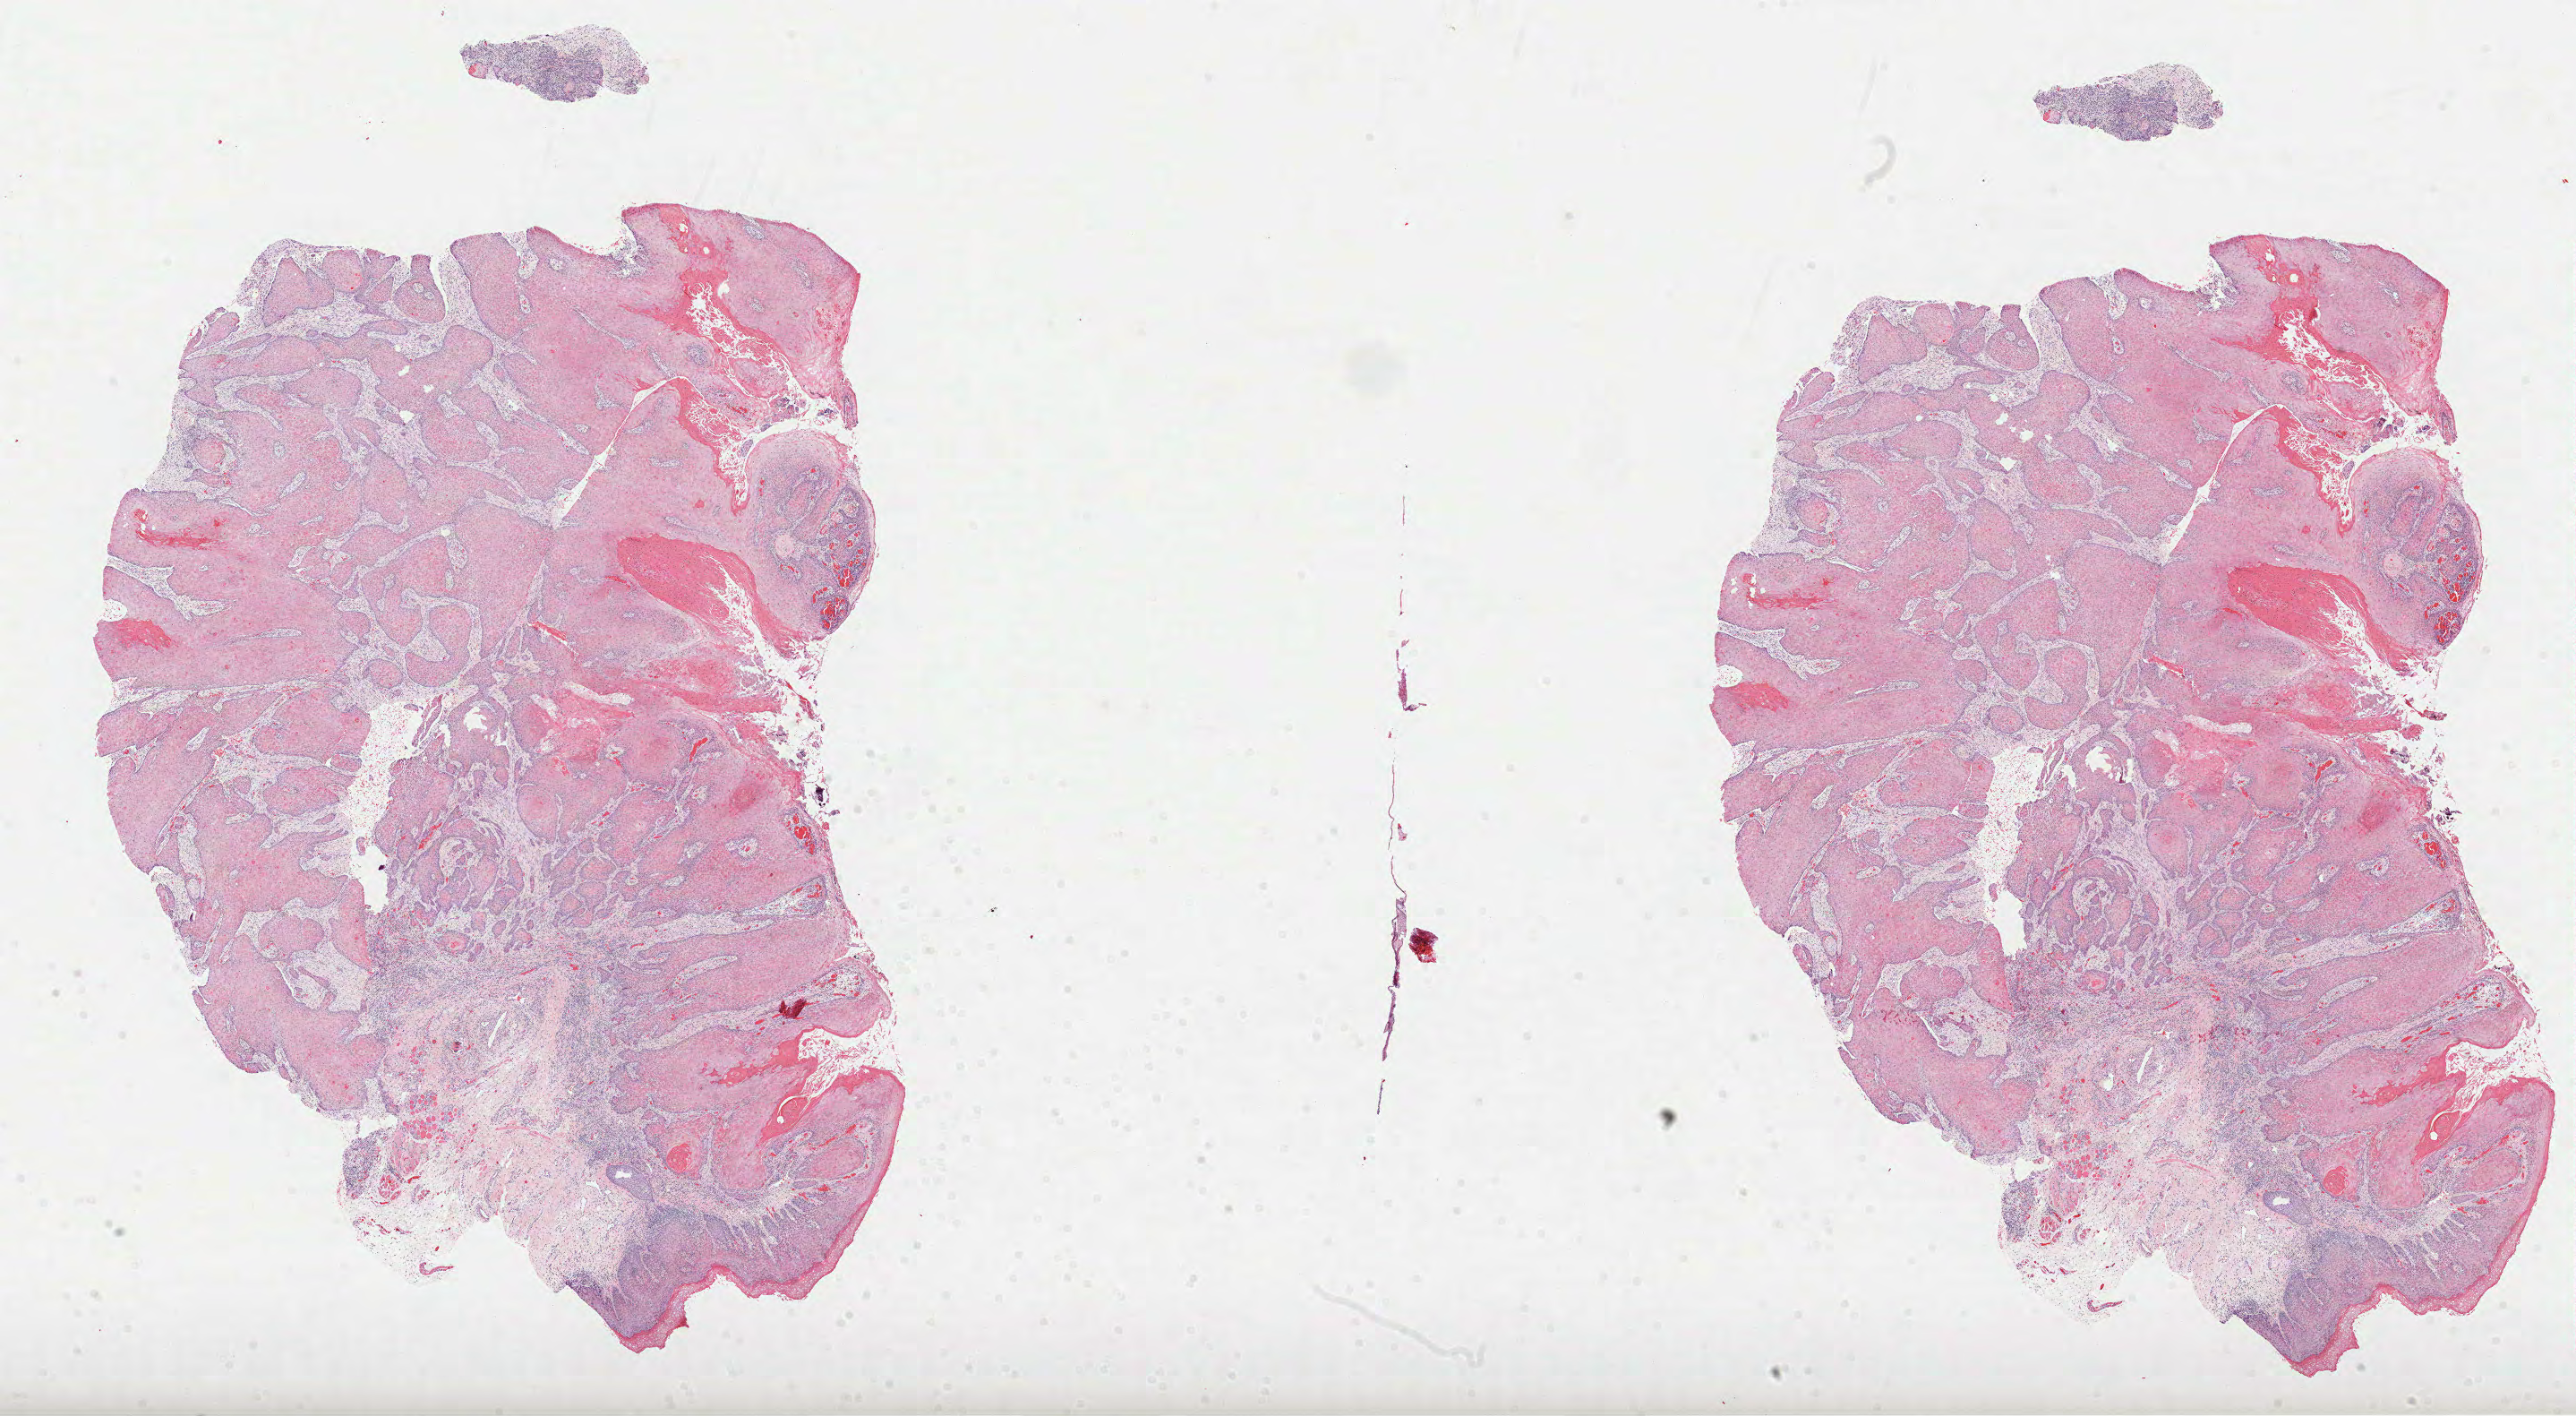
Whole-slide histology image, H&E-stained — low-resolution overview of the scanned area, about 23.2 x 12.8 mm (acquisition: 40x scan), formalin-fixed paraffin-embedded (FFPE) diagnostic section, primary tumour sample from the head and neck. Patient: female, age at initial diagnosis 55 years. Histologic grade: G1 (well differentiated).
• AJCC pathologic stage: I (7th edition)
• diagnosis: Squamous cell carcinoma, NOS (floor of mouth, NOS)